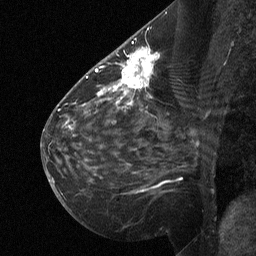
Breast MRI (dynamic contrast-enhanced), one sagittal slice. Slice 34 of 64 in the series (ordered by position). Dynamic contrast-enhanced study with each time point stored as its own series, time point 2 of 3 at this slice position (early post-contrast, ordered by acquisition time). 1.5 T. TE 4.8 ms, TR 27 ms. 256 × 256 image matrix, field of view 200 × 200 mm. Female patient, age 51 years. Case-level facts recorded for this patient, not image findings: setting: breast cancer imaged before/during neoadjuvant chemotherapy; receptor status: HR-positive, HER2-negative.
Outlined on this slice (semi-automatically segmented with operator editing):
- analysis volume of interest (the breast-tissue region the enhancement analysis was run in; not a lesion): bounding box (x1, y1, x2, y2) in pixels: (112, 46, 158, 106)
- tumour enhancement mask (voxels above the 90 % enhancement threshold inside the analysis volume of interest): (112, 48, 157, 105)